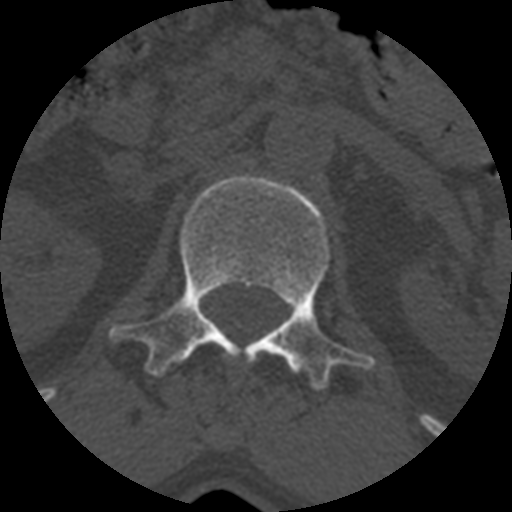
CT including the spine, one axial slice. Position 361 of 399 along the scan axis. Bone window (W 1800 / L 400 HU). 1.25 mm slice thickness. 512 × 512 image matrix, field of view 160 × 160 mm. Patient age 71 years. Case-level facts recorded for this patient, not image findings: primary cancer: prostate.
Outlined on this slice (semi-automatic segmentation, software-assisted and operator-edited):
- L1 vertebra: bounding box [x1, y1, x2, y2] px = [111, 177, 373, 393]